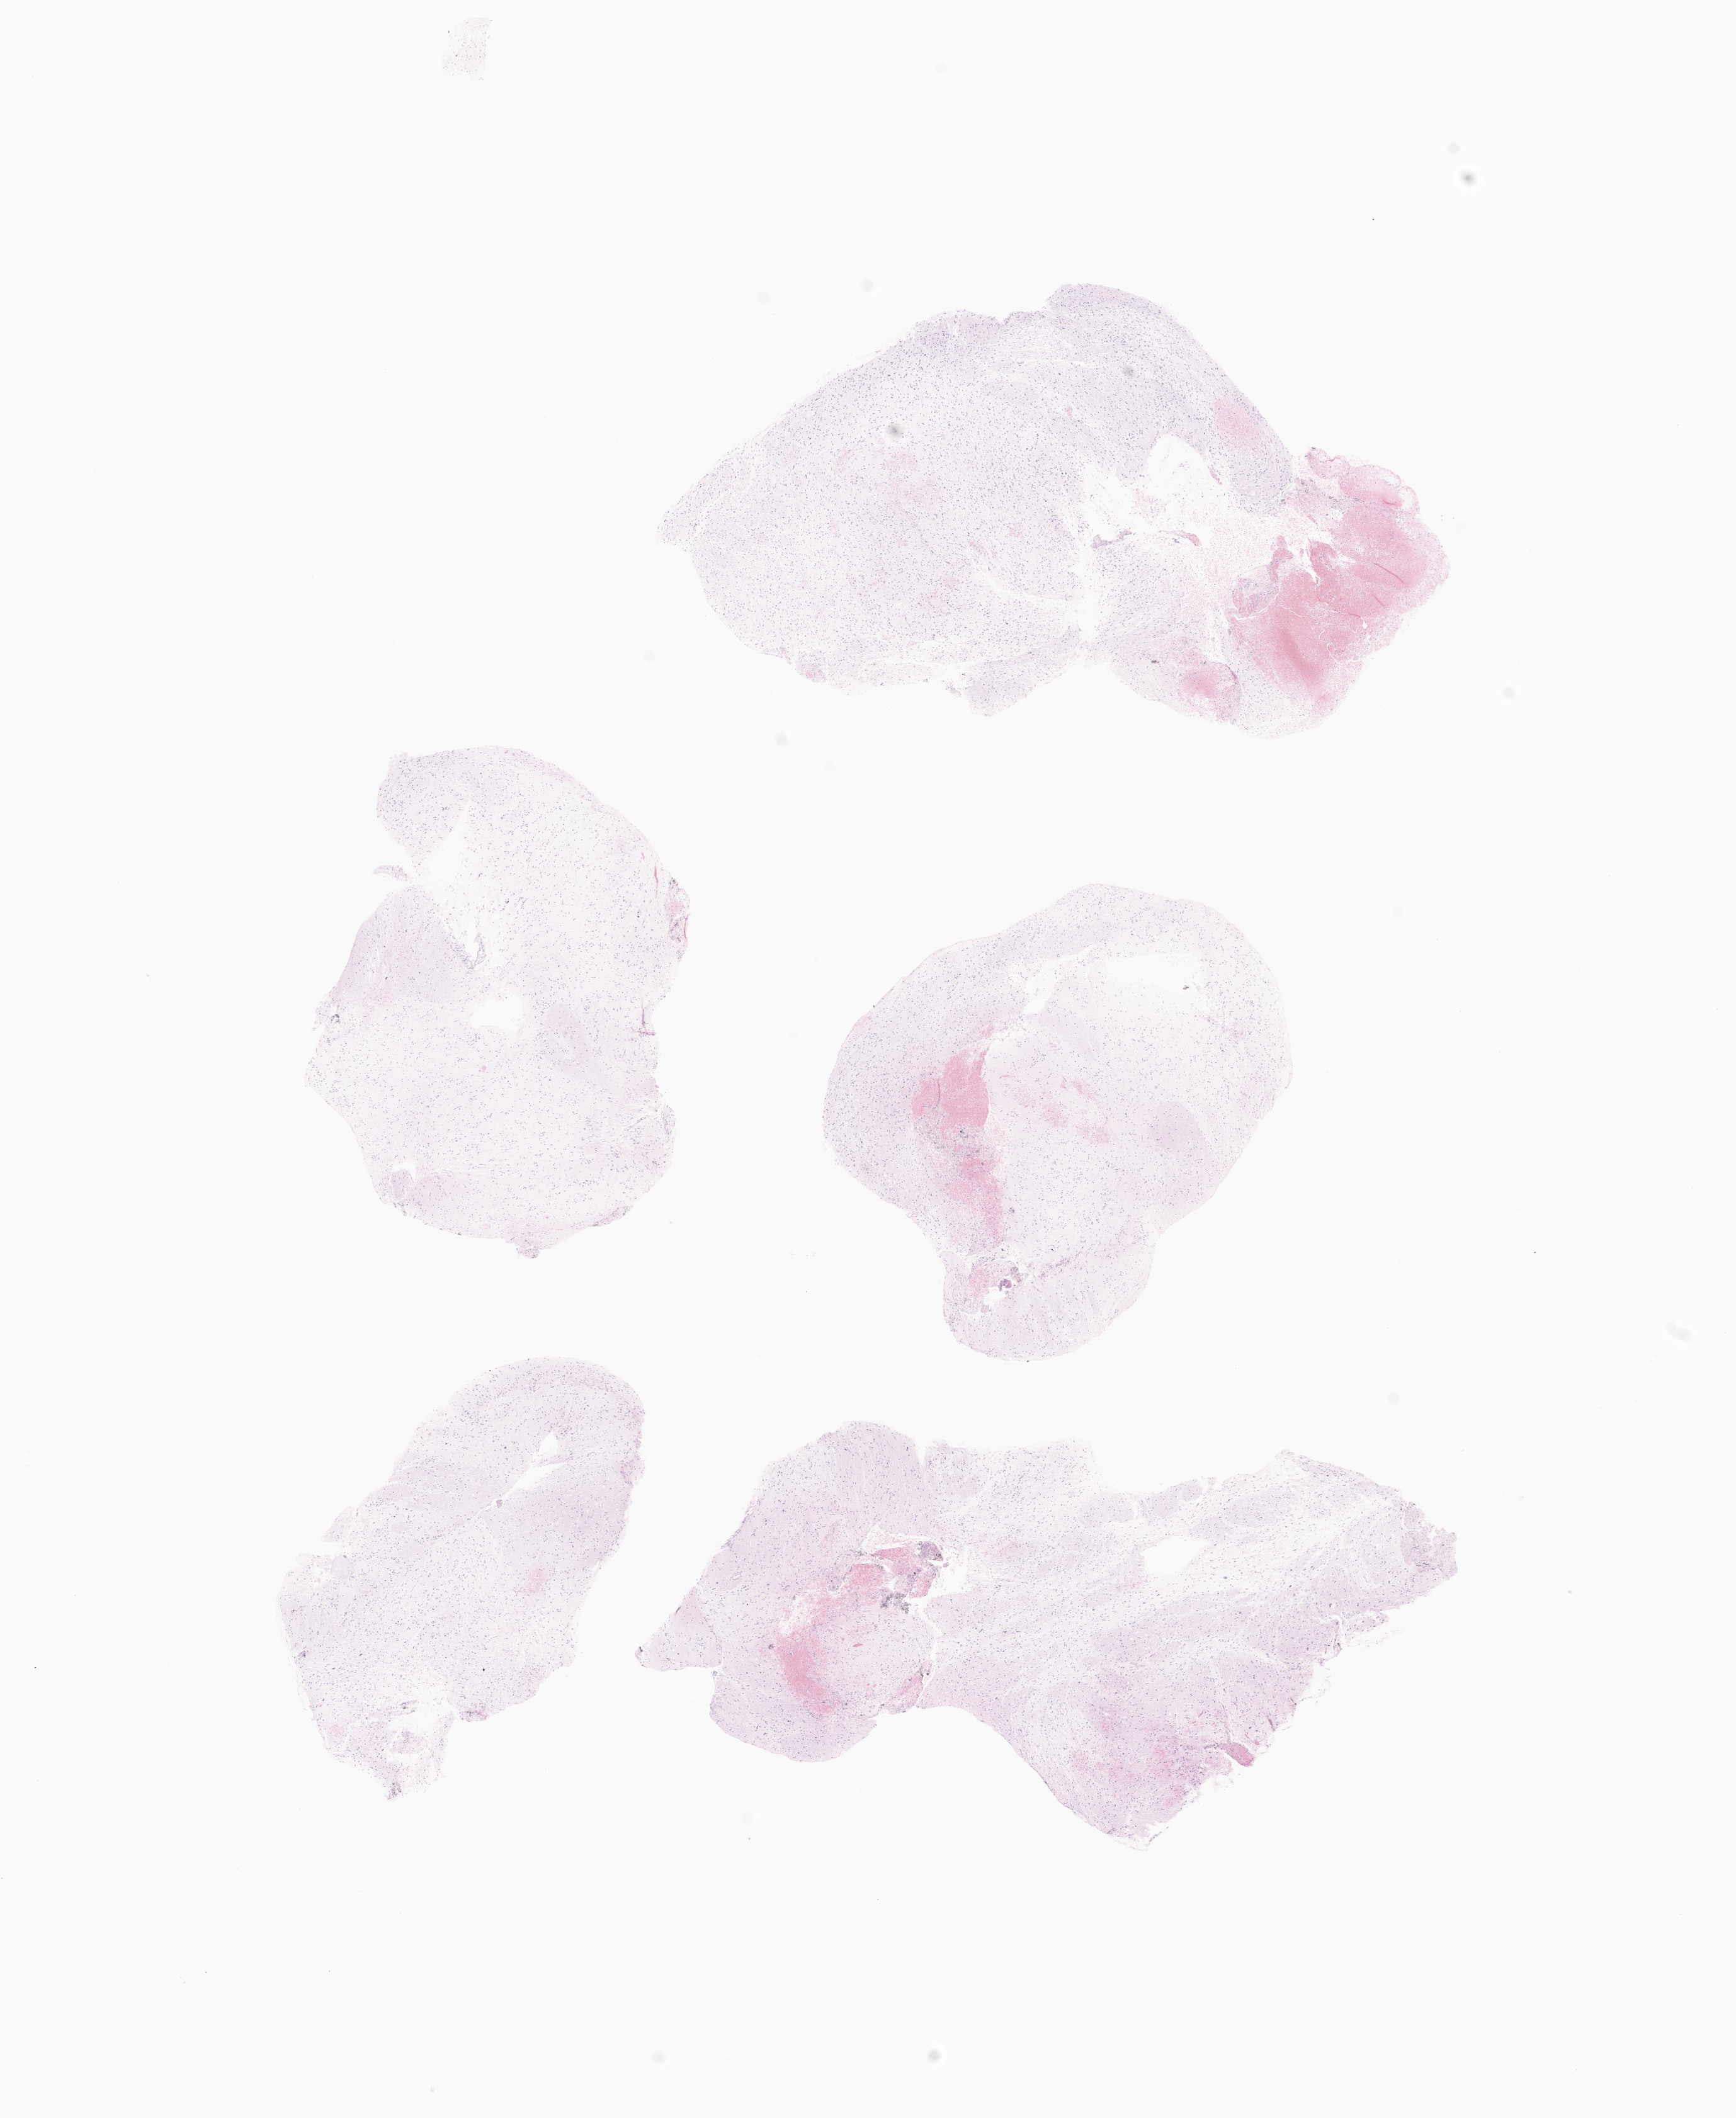
H&E whole-slide image of tumor tissue from the brain stem, a low-resolution overview of the entire scanned area, about 11.6 x 14.2 mm; formalin-fixed, paraffin-embedded (FFPE) tissue. Patient: male, age 62 months (5 years 2 months).
Diagnosis (ICD-O-3 morphology term): Neoplasm, uncertain whether benign or malignant.